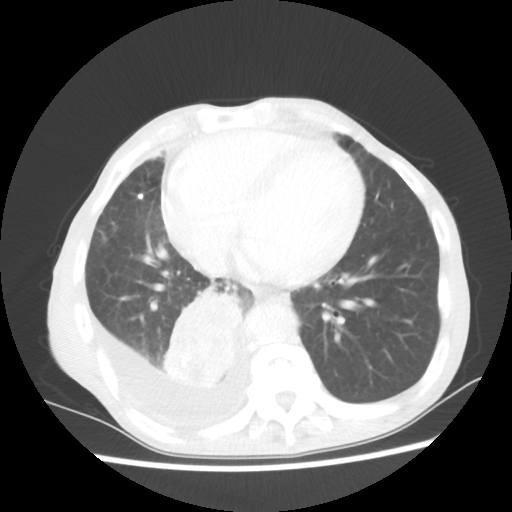
Chest CT, one axial slice; slice 22 of 60 in the series (ordered by position); reconstruction kernel STANDARD; 80 kVp; lung window (W 1500 / L -600 HU); 5 mm slice thickness; 512 × 512 image matrix, field of view 335 × 335 mm. Male patient, age 76 years. Case-level facts recorded for this patient, not image findings: clinical TNM (as recorded): T3 N3 M1a; histopathological grade: G3.
Annotated regions visible in this slice (bounding box drawn by a radiologist):
- lung tumour (recorded histology: squamous cell carcinoma): bounding box <162,284,248,393> (left, top, right, bottom; pixels)